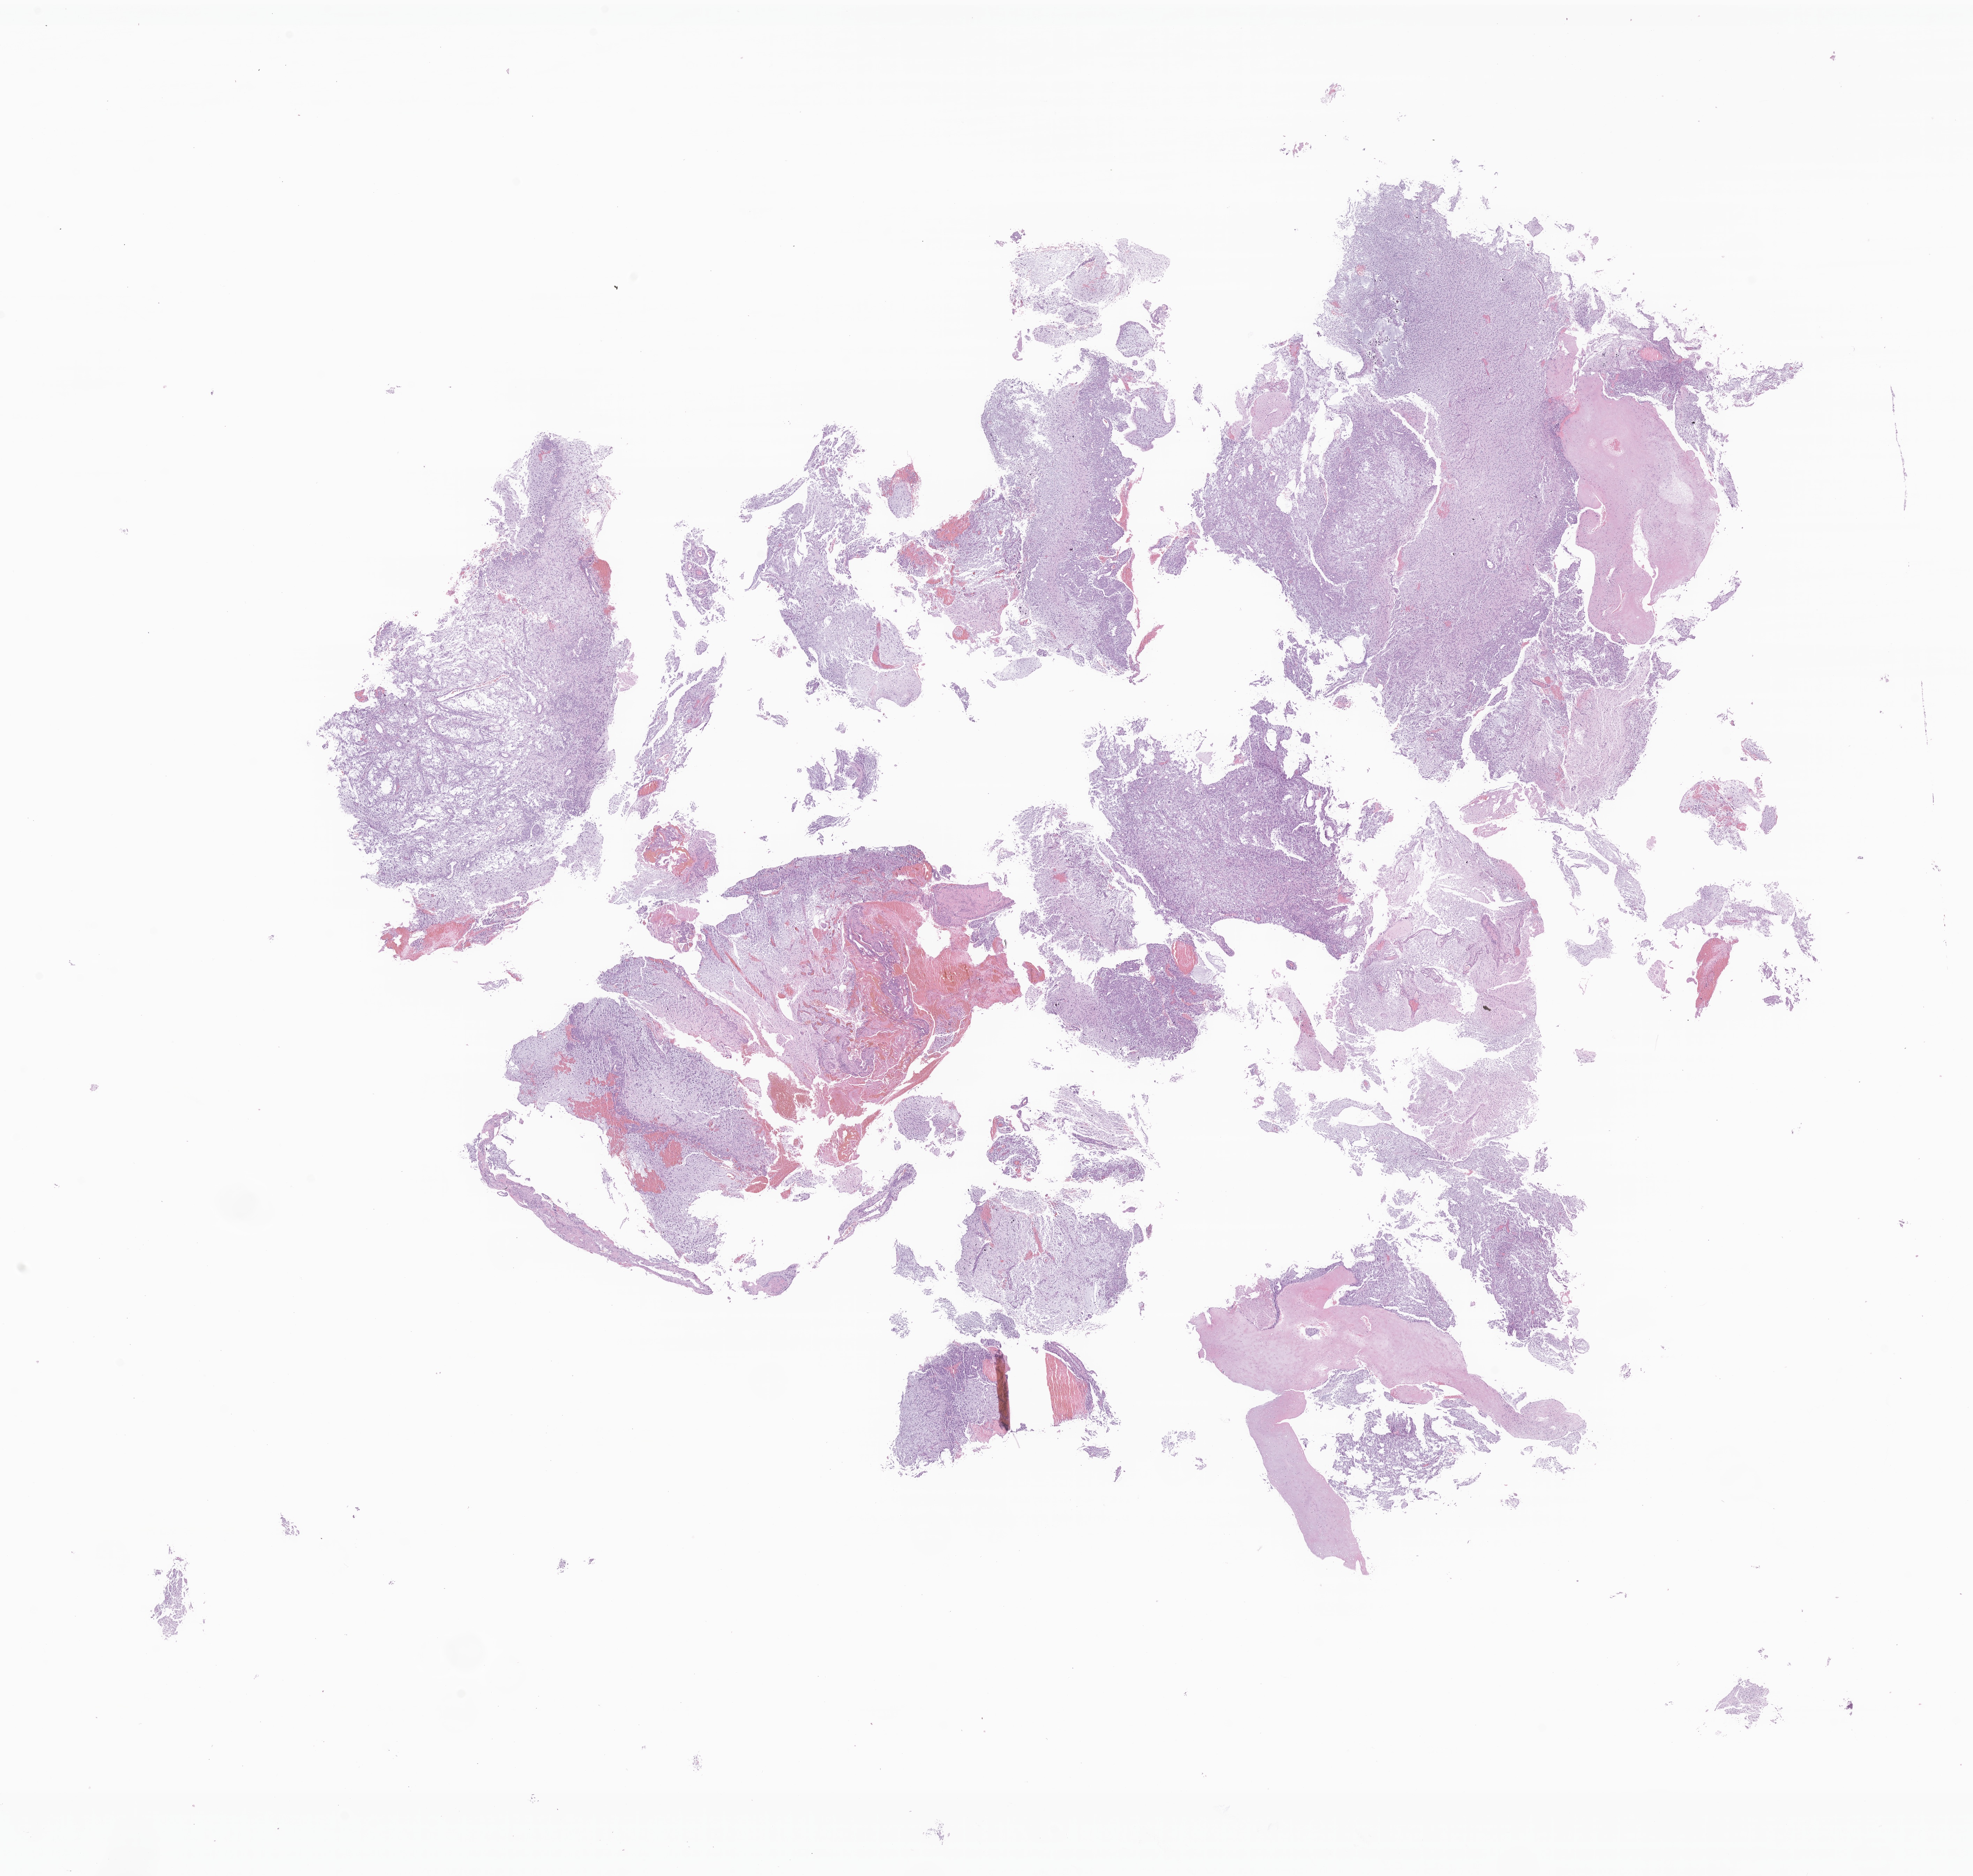
Haematoxylin and eosin whole-slide image of tumor tissue from the frontal lobe — a low-resolution overview of the entire scanned area, about 23.8 x 22.7 mm, FFPE section. Patient male; age 163 months (13 years 7 months).
Recorded diagnosis: Pilocytic astrocytoma.